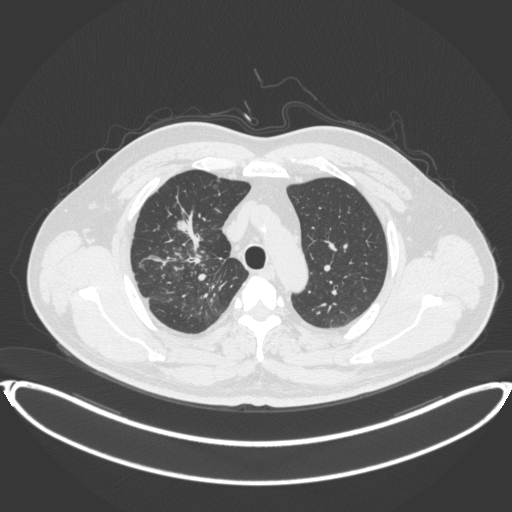
Chest CT, one axial slice; position 296 of 399 along the scan axis; reconstruction kernel B31f; lung window (W 1500 / L -600 HU); 1 mm slice thickness; 512 × 512 image matrix, field of view 445 × 445 mm. Patient: male, 53 years. From the clinical record (not read from this slice): clinical TNM (as recorded): T2a N0 M0.
Structures marked on this image (bounding box drawn by a radiologist):
- lung tumour (recorded histology: adenocarcinoma): bounding box <171,210,196,243> (left, top, right, bottom; pixels)